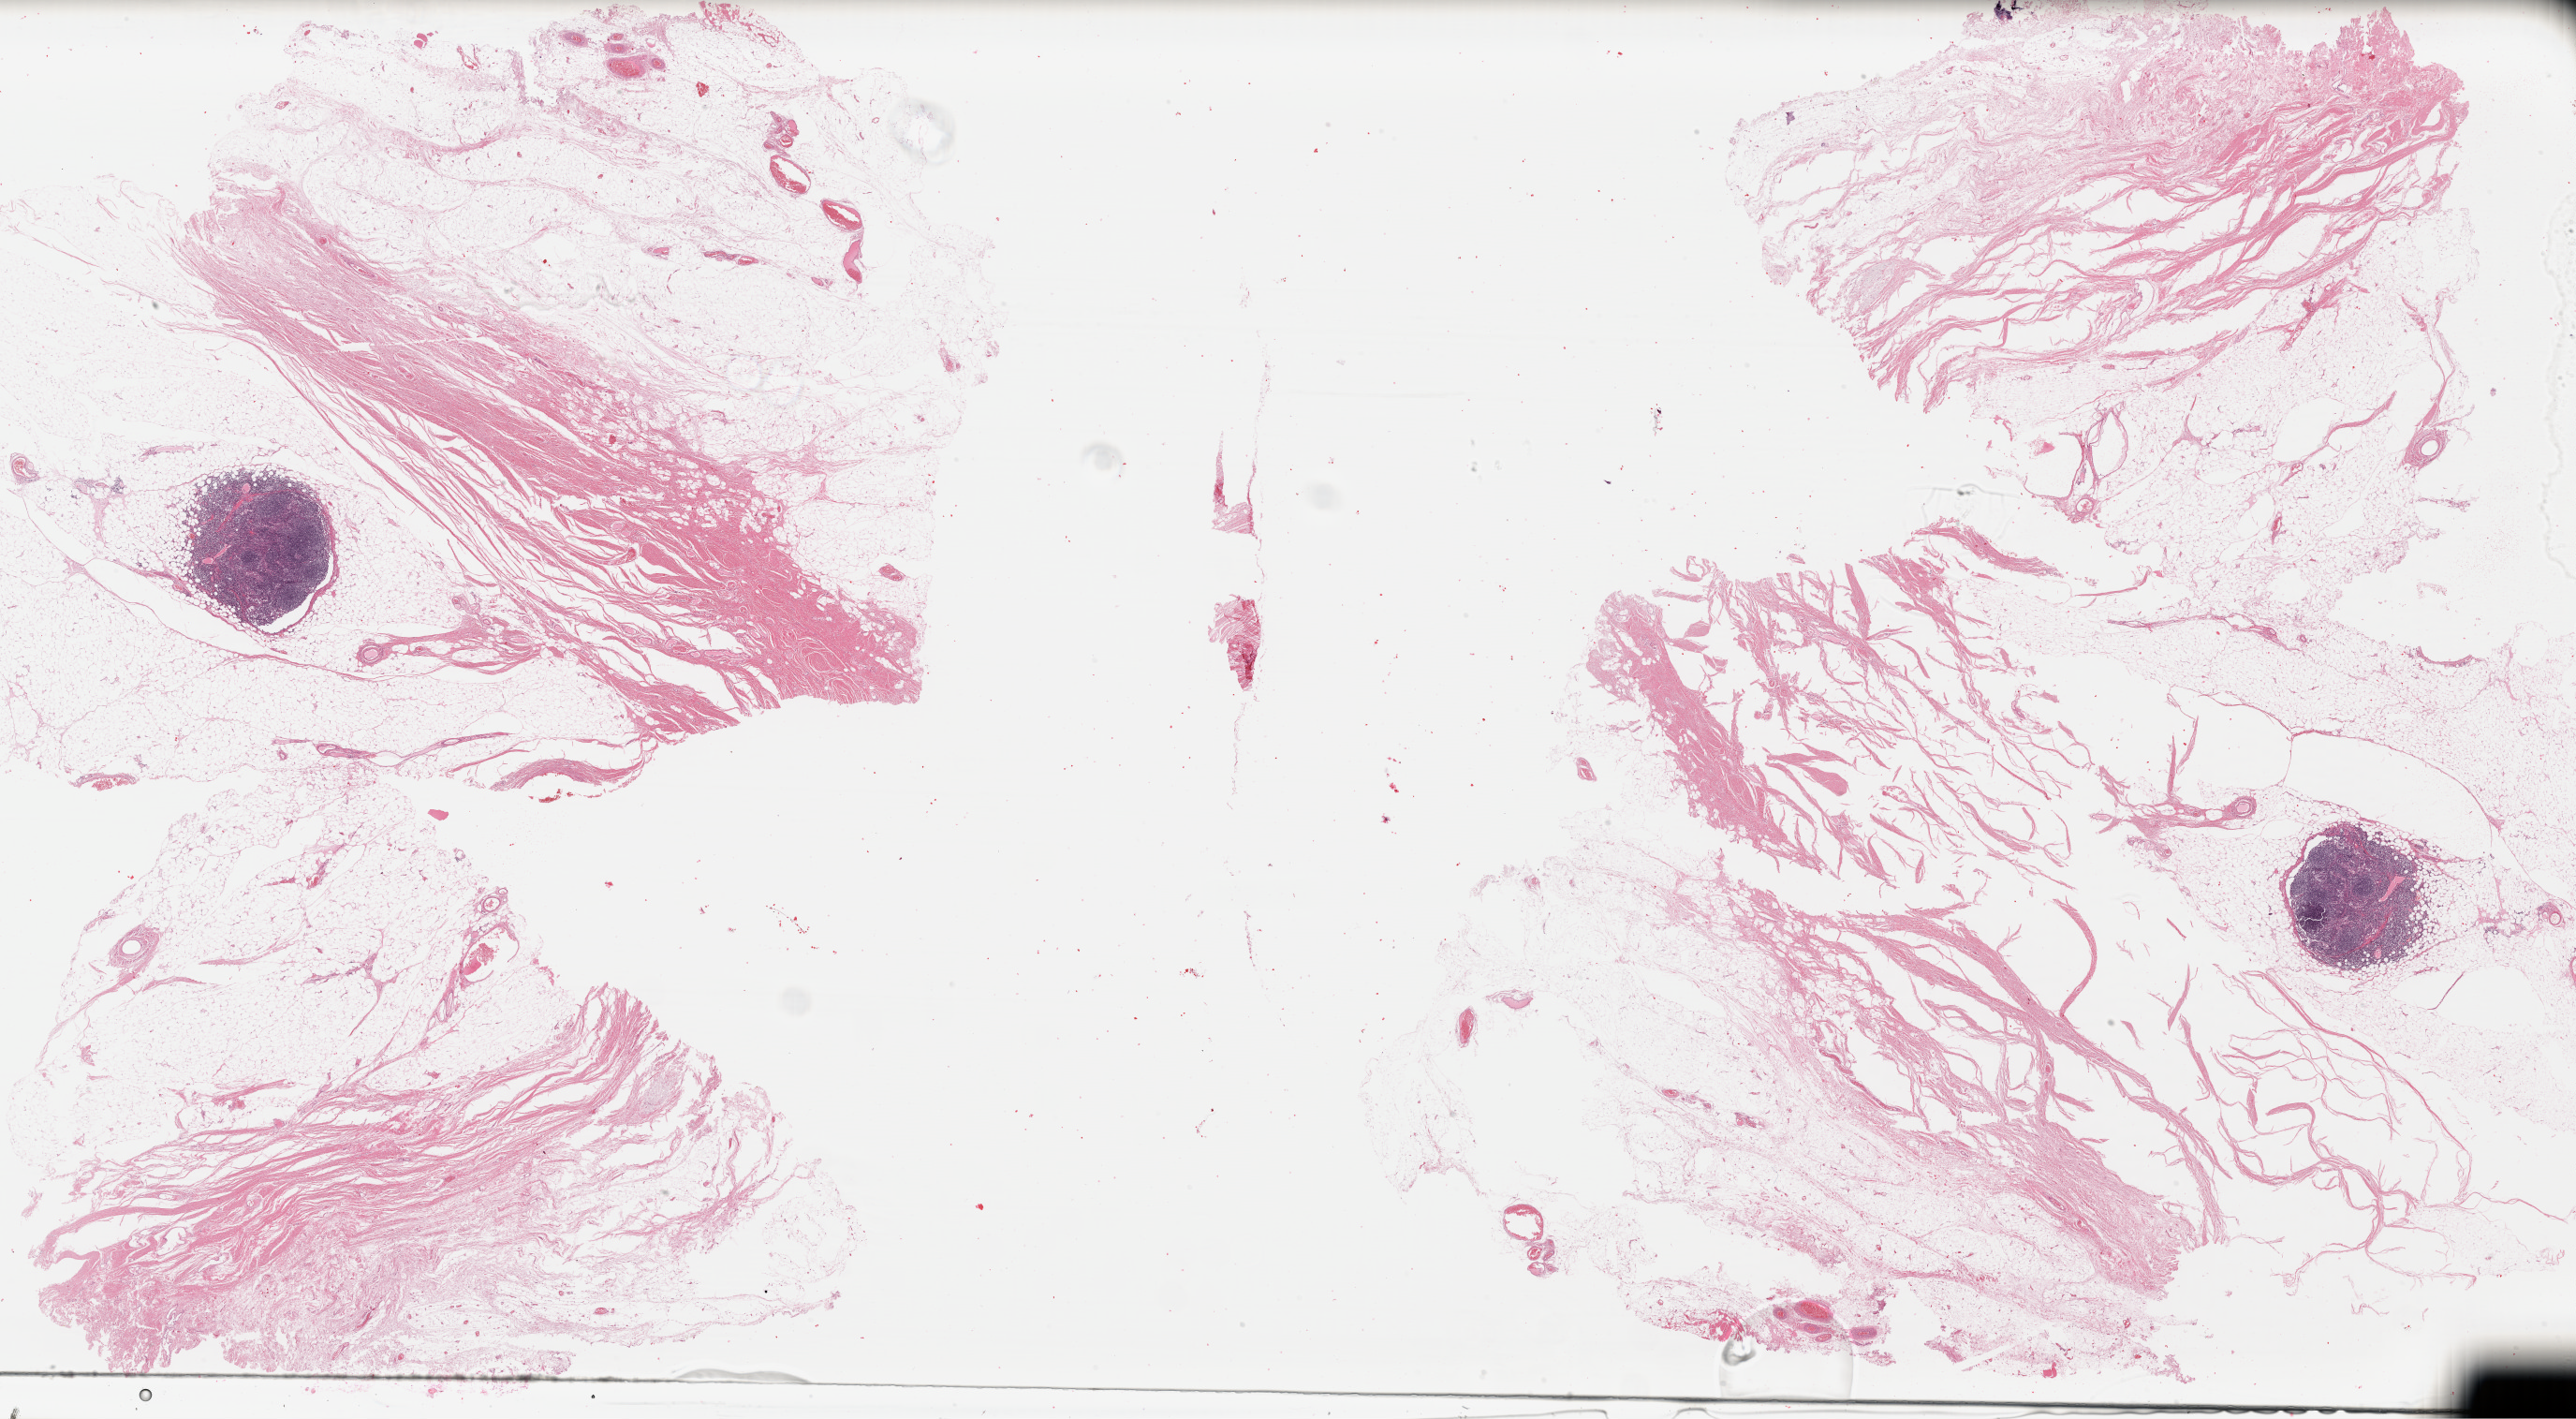
Whole-slide histology image, Hematoxylin and eosin (H&E) stained, whole scanned area (about 43.3 x 23.8 mm, slide scanned at 40x) shown as a low-resolution overview. Formalin-fixed paraffin-embedded (FFPE) diagnostic section. Metastatic tumour sample, sampled site: lymph node. Male patient; age at initial diagnosis 65 years.
This section: metastatic tumour tissue. Patient diagnosis: Malignant melanoma, NOS.